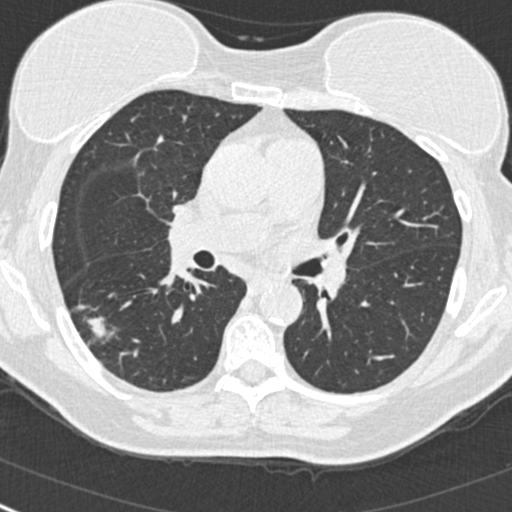
Low-dose screening chest CT, one axial slice; position 151 of 268 along the scan axis; reconstruction kernel B30f; 120 kVp; lung window (W 1500 / L -600 HU); 512 × 512 image matrix, field of view 296 × 296 mm.
Annotated regions visible in this slice (expert manual segmentation):
- lesion 1 (tumor, upper lobe of right lung): bounding box (x1, y1, x2, y2) in pixels: (88, 319, 110, 337)